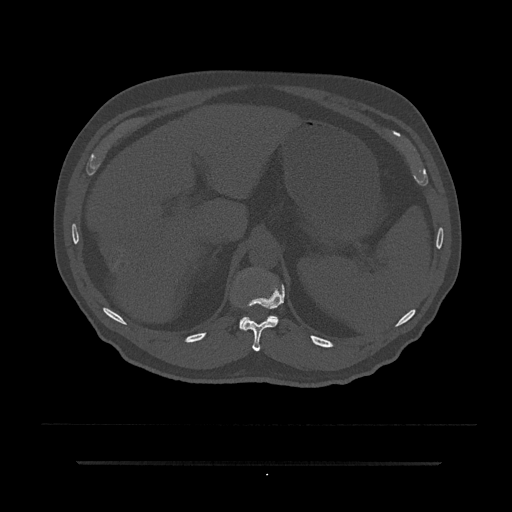
CT including the spine, one axial slice. Slice 247 of 797 in the series (ordered by position). 120 kVp. Bone window (W 1800 / L 400 HU). 512 × 512 image matrix. Patient: male, 59 years. Case-level facts recorded for this patient, not image findings: primary cancer: bile ducts.
Annotated regions visible in this slice (semi-automatic segmentation, software-assisted and operator-edited):
- T11 vertebra: bounding box <241,283,284,352> (left, top, right, bottom; pixels)
- T12 vertebra: <239,315,279,331>